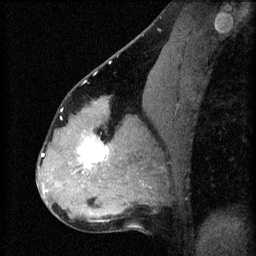
Breast MRI (dynamic contrast-enhanced), one sagittal slice. Slice 33 of 60 in the series (ordered by position). 3 images stored at this slice position (order not interpretable as contrast timing). 1.5 T. TE 4.2 ms, TR 8.2 ms. 2.3 mm slice thickness. 256 × 256 image matrix. Patient: female, 37 years.
Outlined on this slice (semi-automatically segmented with operator editing):
- analysis volume of interest (the breast-tissue region the enhancement analysis was run in; not a lesion): bounding box <67,120,122,179> (left, top, right, bottom; pixels)
- tumour enhancement mask (voxels above the 70 % enhancement threshold inside the analysis volume of interest): <79,136,109,169>